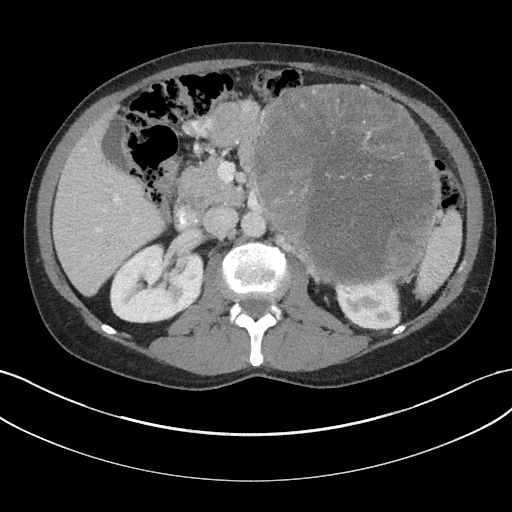
Contrast-enhanced abdominal CT, one axial slice. Position 101 of 147 along the scan axis. Reconstruction kernel I31f/3. 100 kVp. Intravenous contrast given. Soft-tissue window (W 400 / L 40 HU). 3 mm slice thickness. 512 × 512 image matrix, field of view 384 × 384 mm. Male patient, age 58 years. Case-level facts recorded for this patient, not image findings: diagnosis: adrenocortical carcinoma; tumour side: left adrenal; tumour size at pathology: 22 cm; Ki-67 index: 26 %; stage (as recorded): 2.
Outlined on this slice (semi-automatically segmented with operator editing):
- mass: box from (x=254, y=85) to (x=434, y=281) px